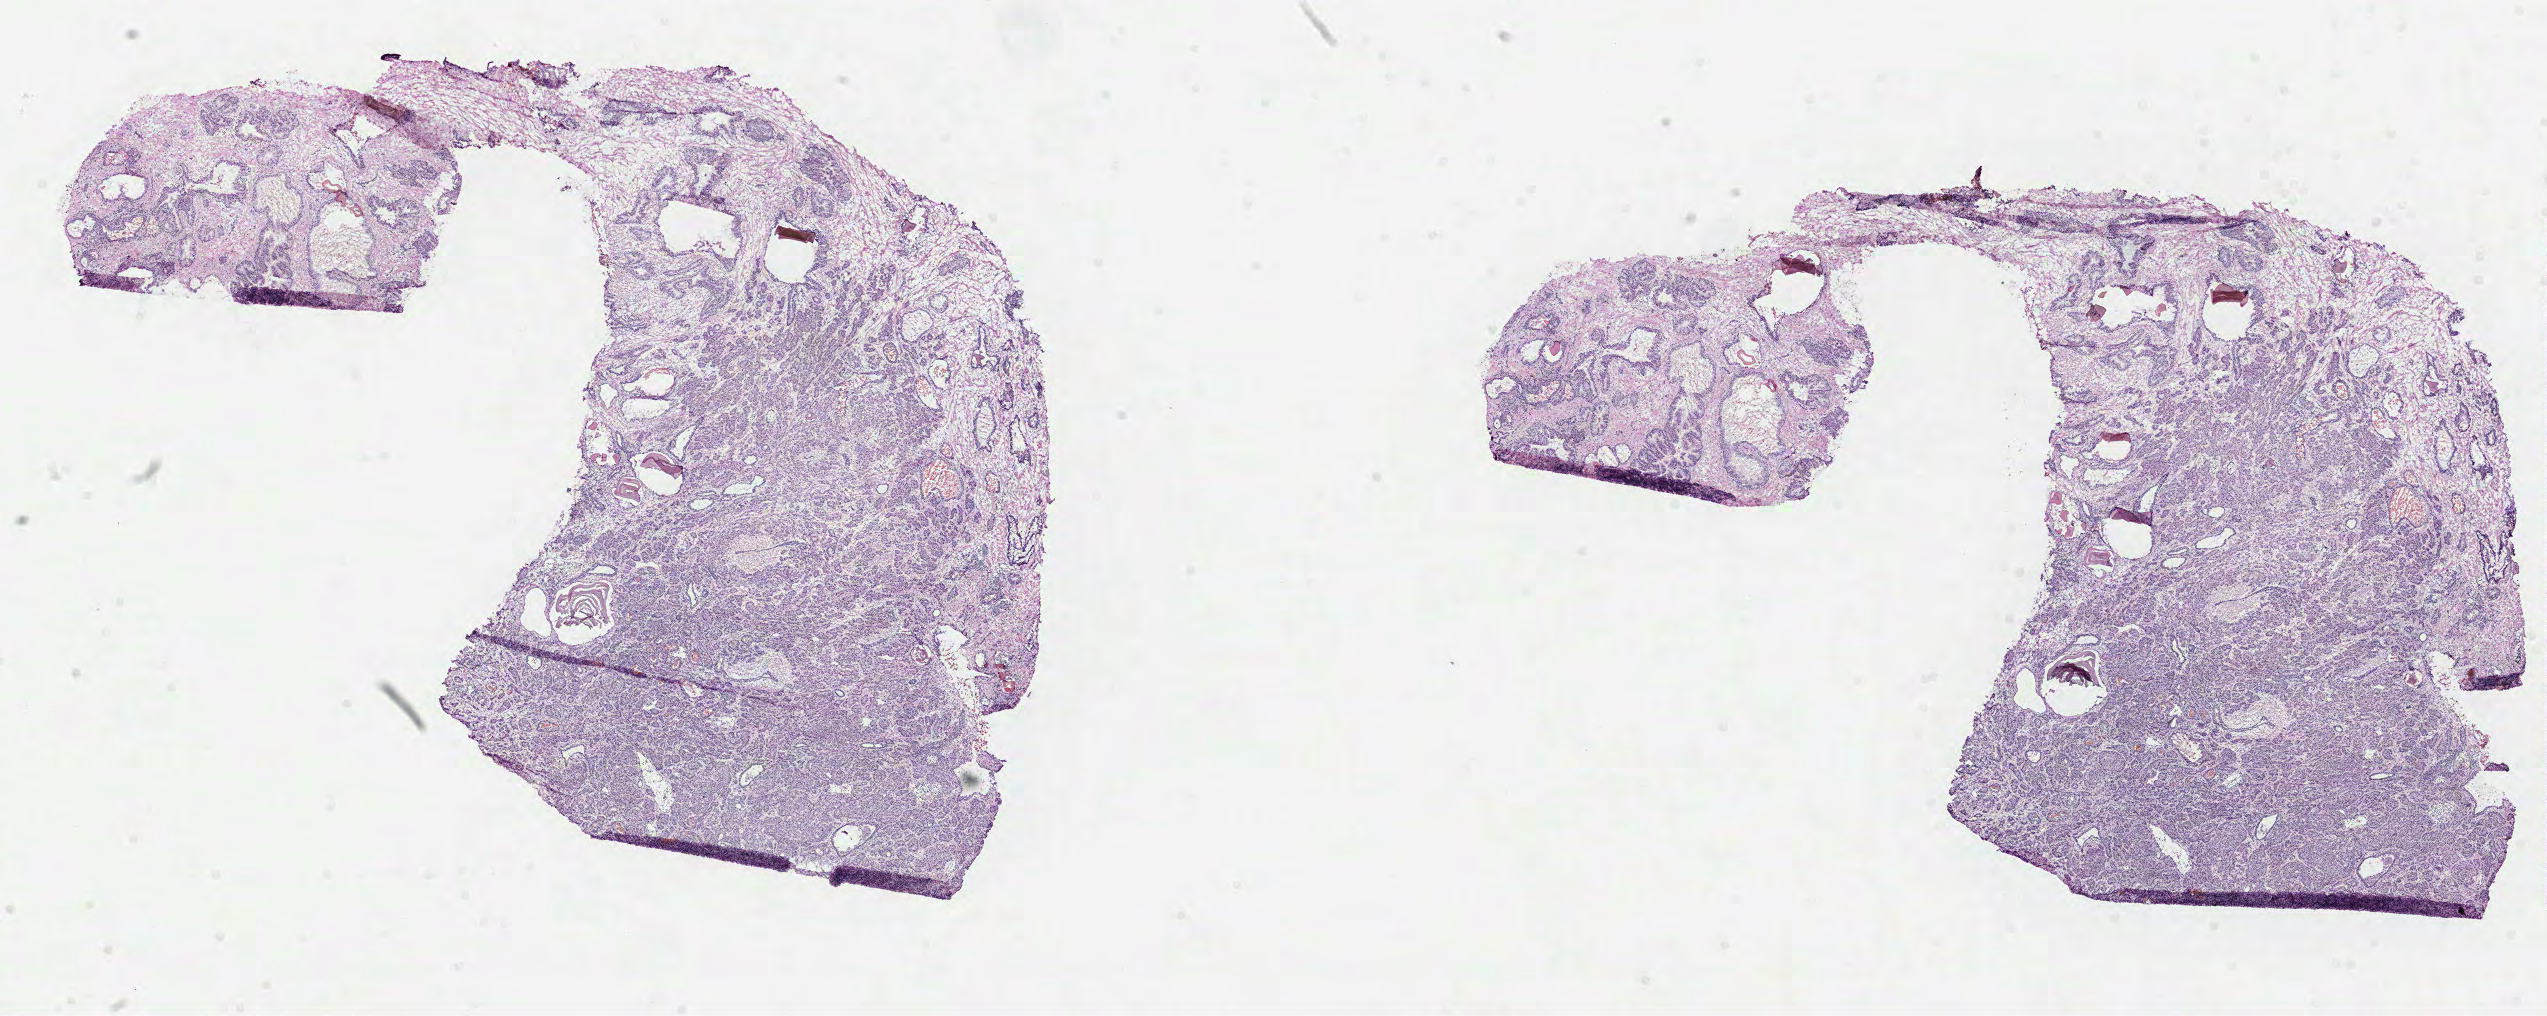
Whole-slide histology image, Hematoxylin and eosin (H&E) stained — a low-resolution overview of the entire scanned area, about 20.5 x 8.2 mm (acquisition: 40x scan); formalin-fixed paraffin-embedded (FFPE) diagnostic section; primary tumour sample from the prostate. Male, age 66 years at initial diagnosis. Gleason score: 8 (4+4).
* laterality: bilateral
* lymph nodes positive (case pathology): 0 of 9 examined
* histologic diagnosis: Acinar cell carcinoma (prostate gland)